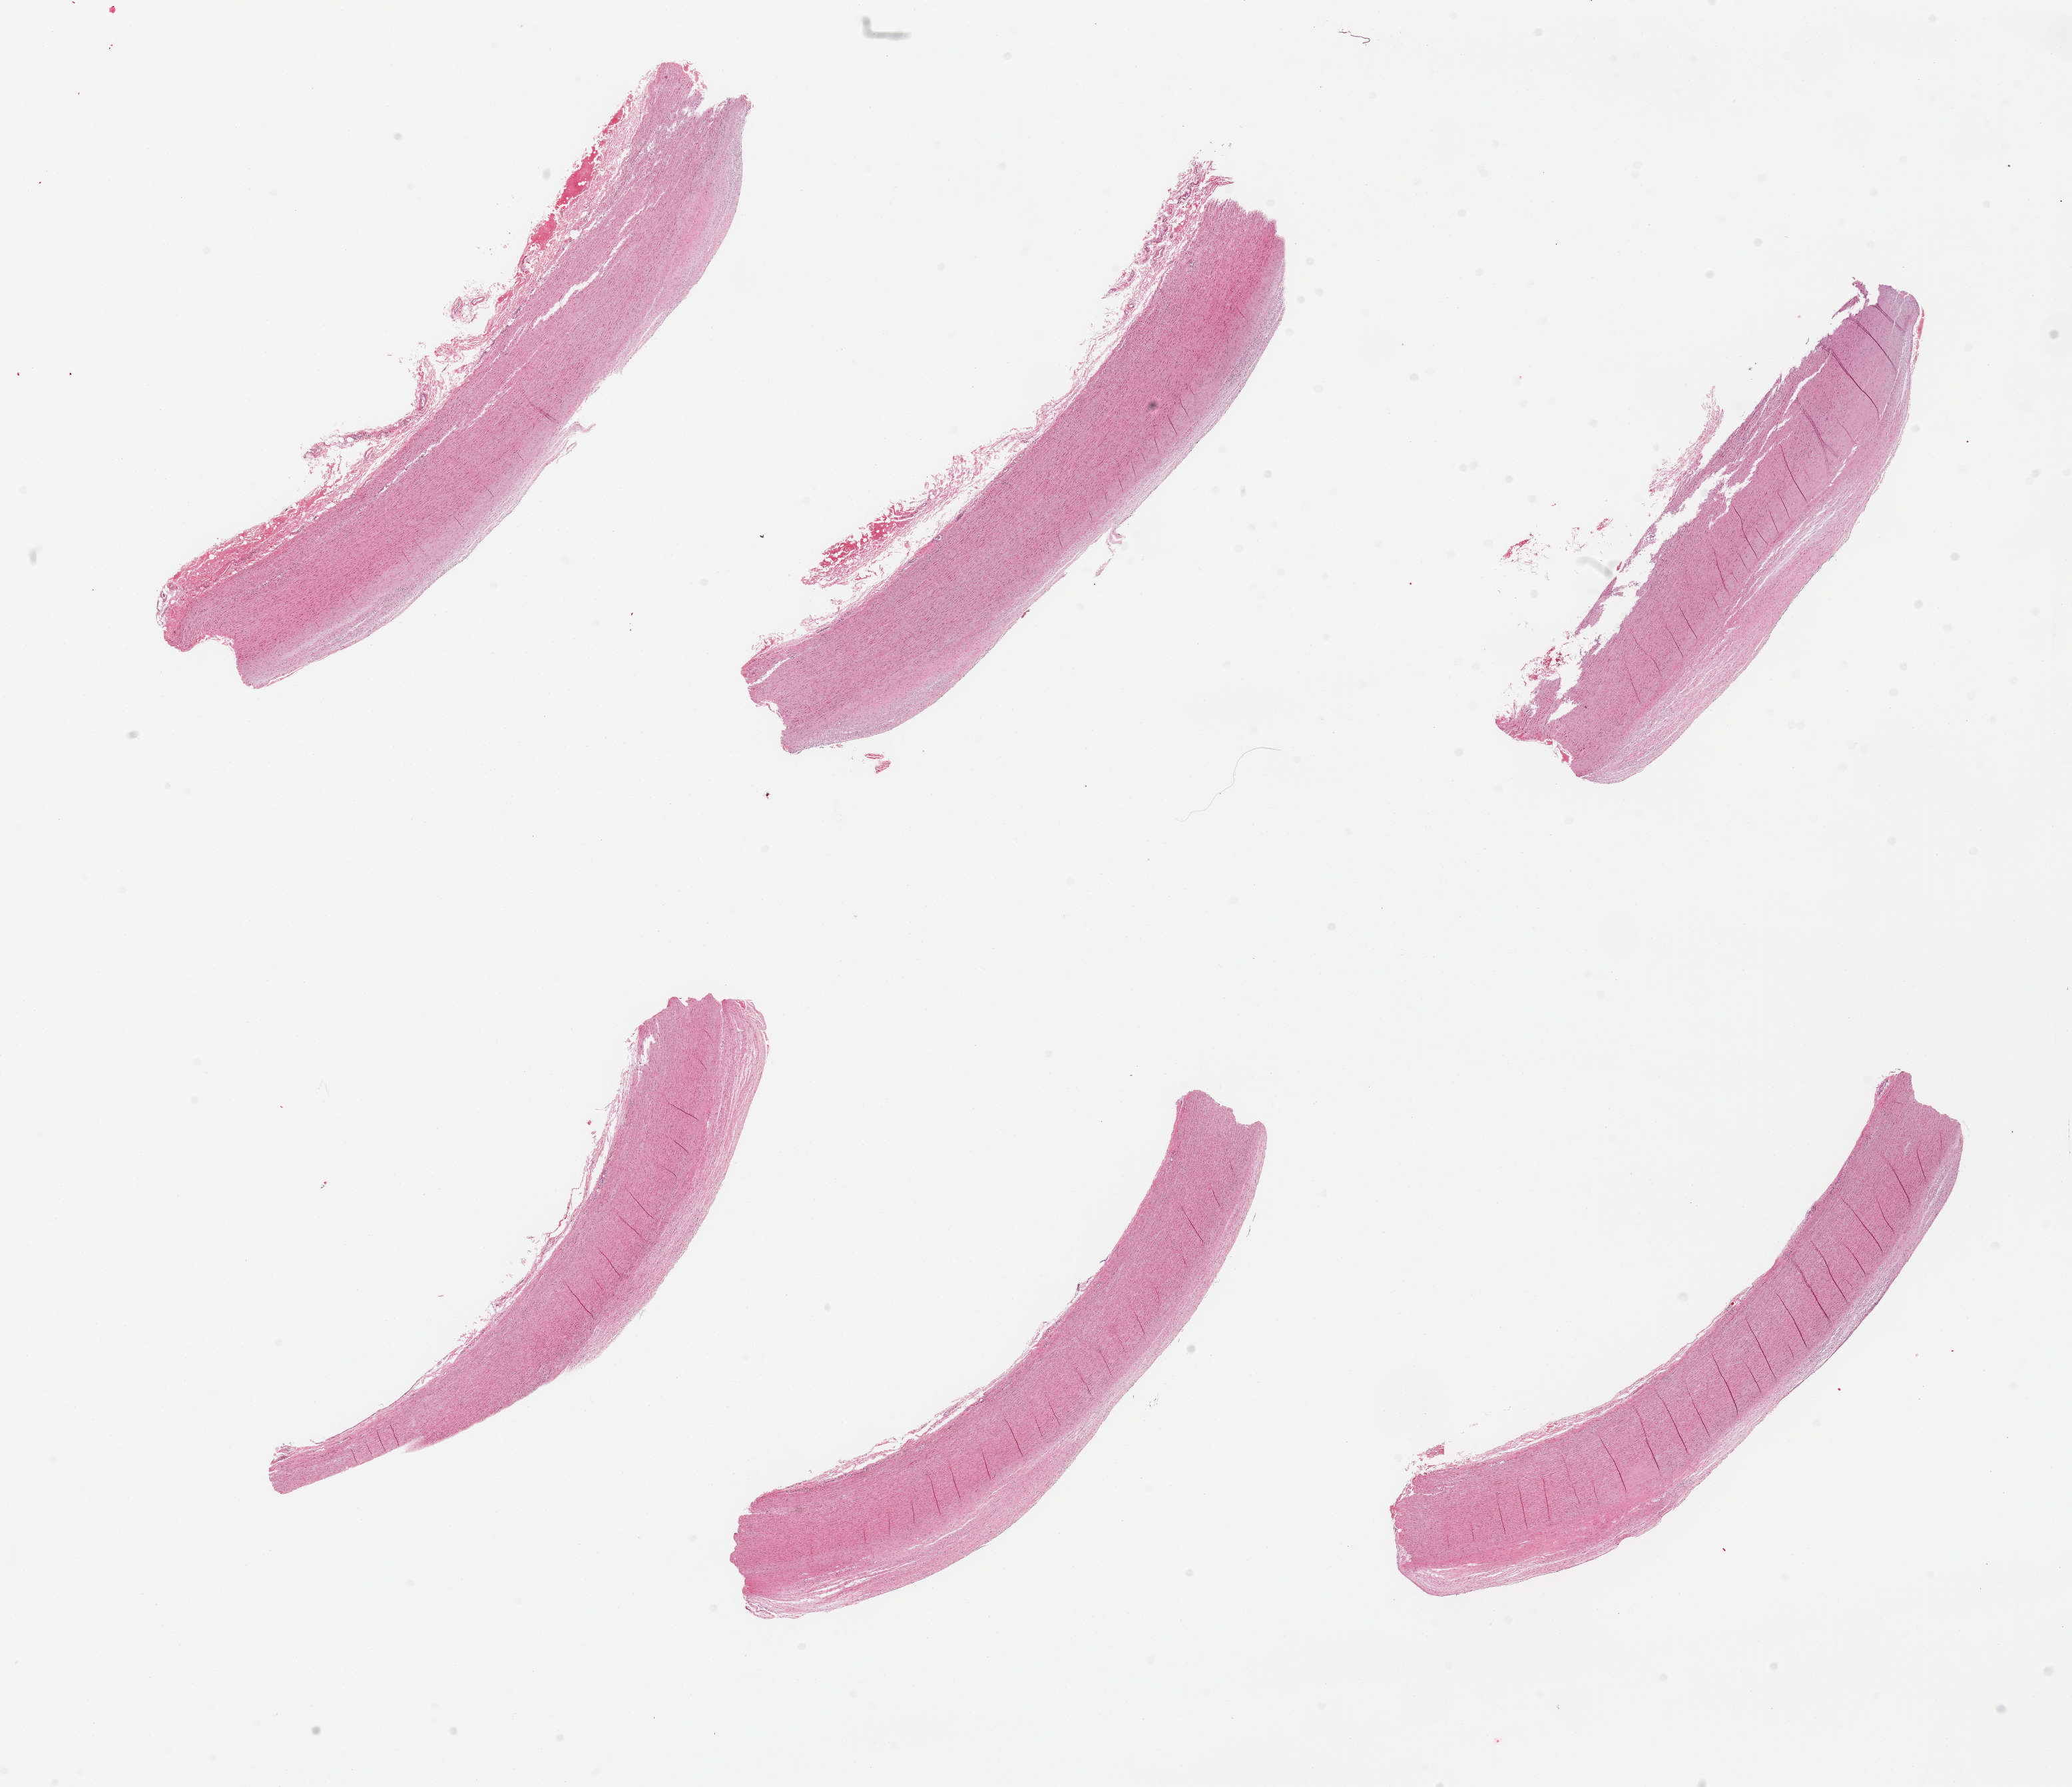
Digitized H&E-stained section — whole scanned area (about 24.6 x 21.2 mm, slide scanned at 20x) shown as a low-resolution overview; PAXgene-fixed, paraffin-embedded tissue; sampled site (target tissue): aorta; tissue donor sample. Donor sex: male.
* reviewer comment on this tissue sample: 6 pieces, atherosis layer up to ~0.5mm